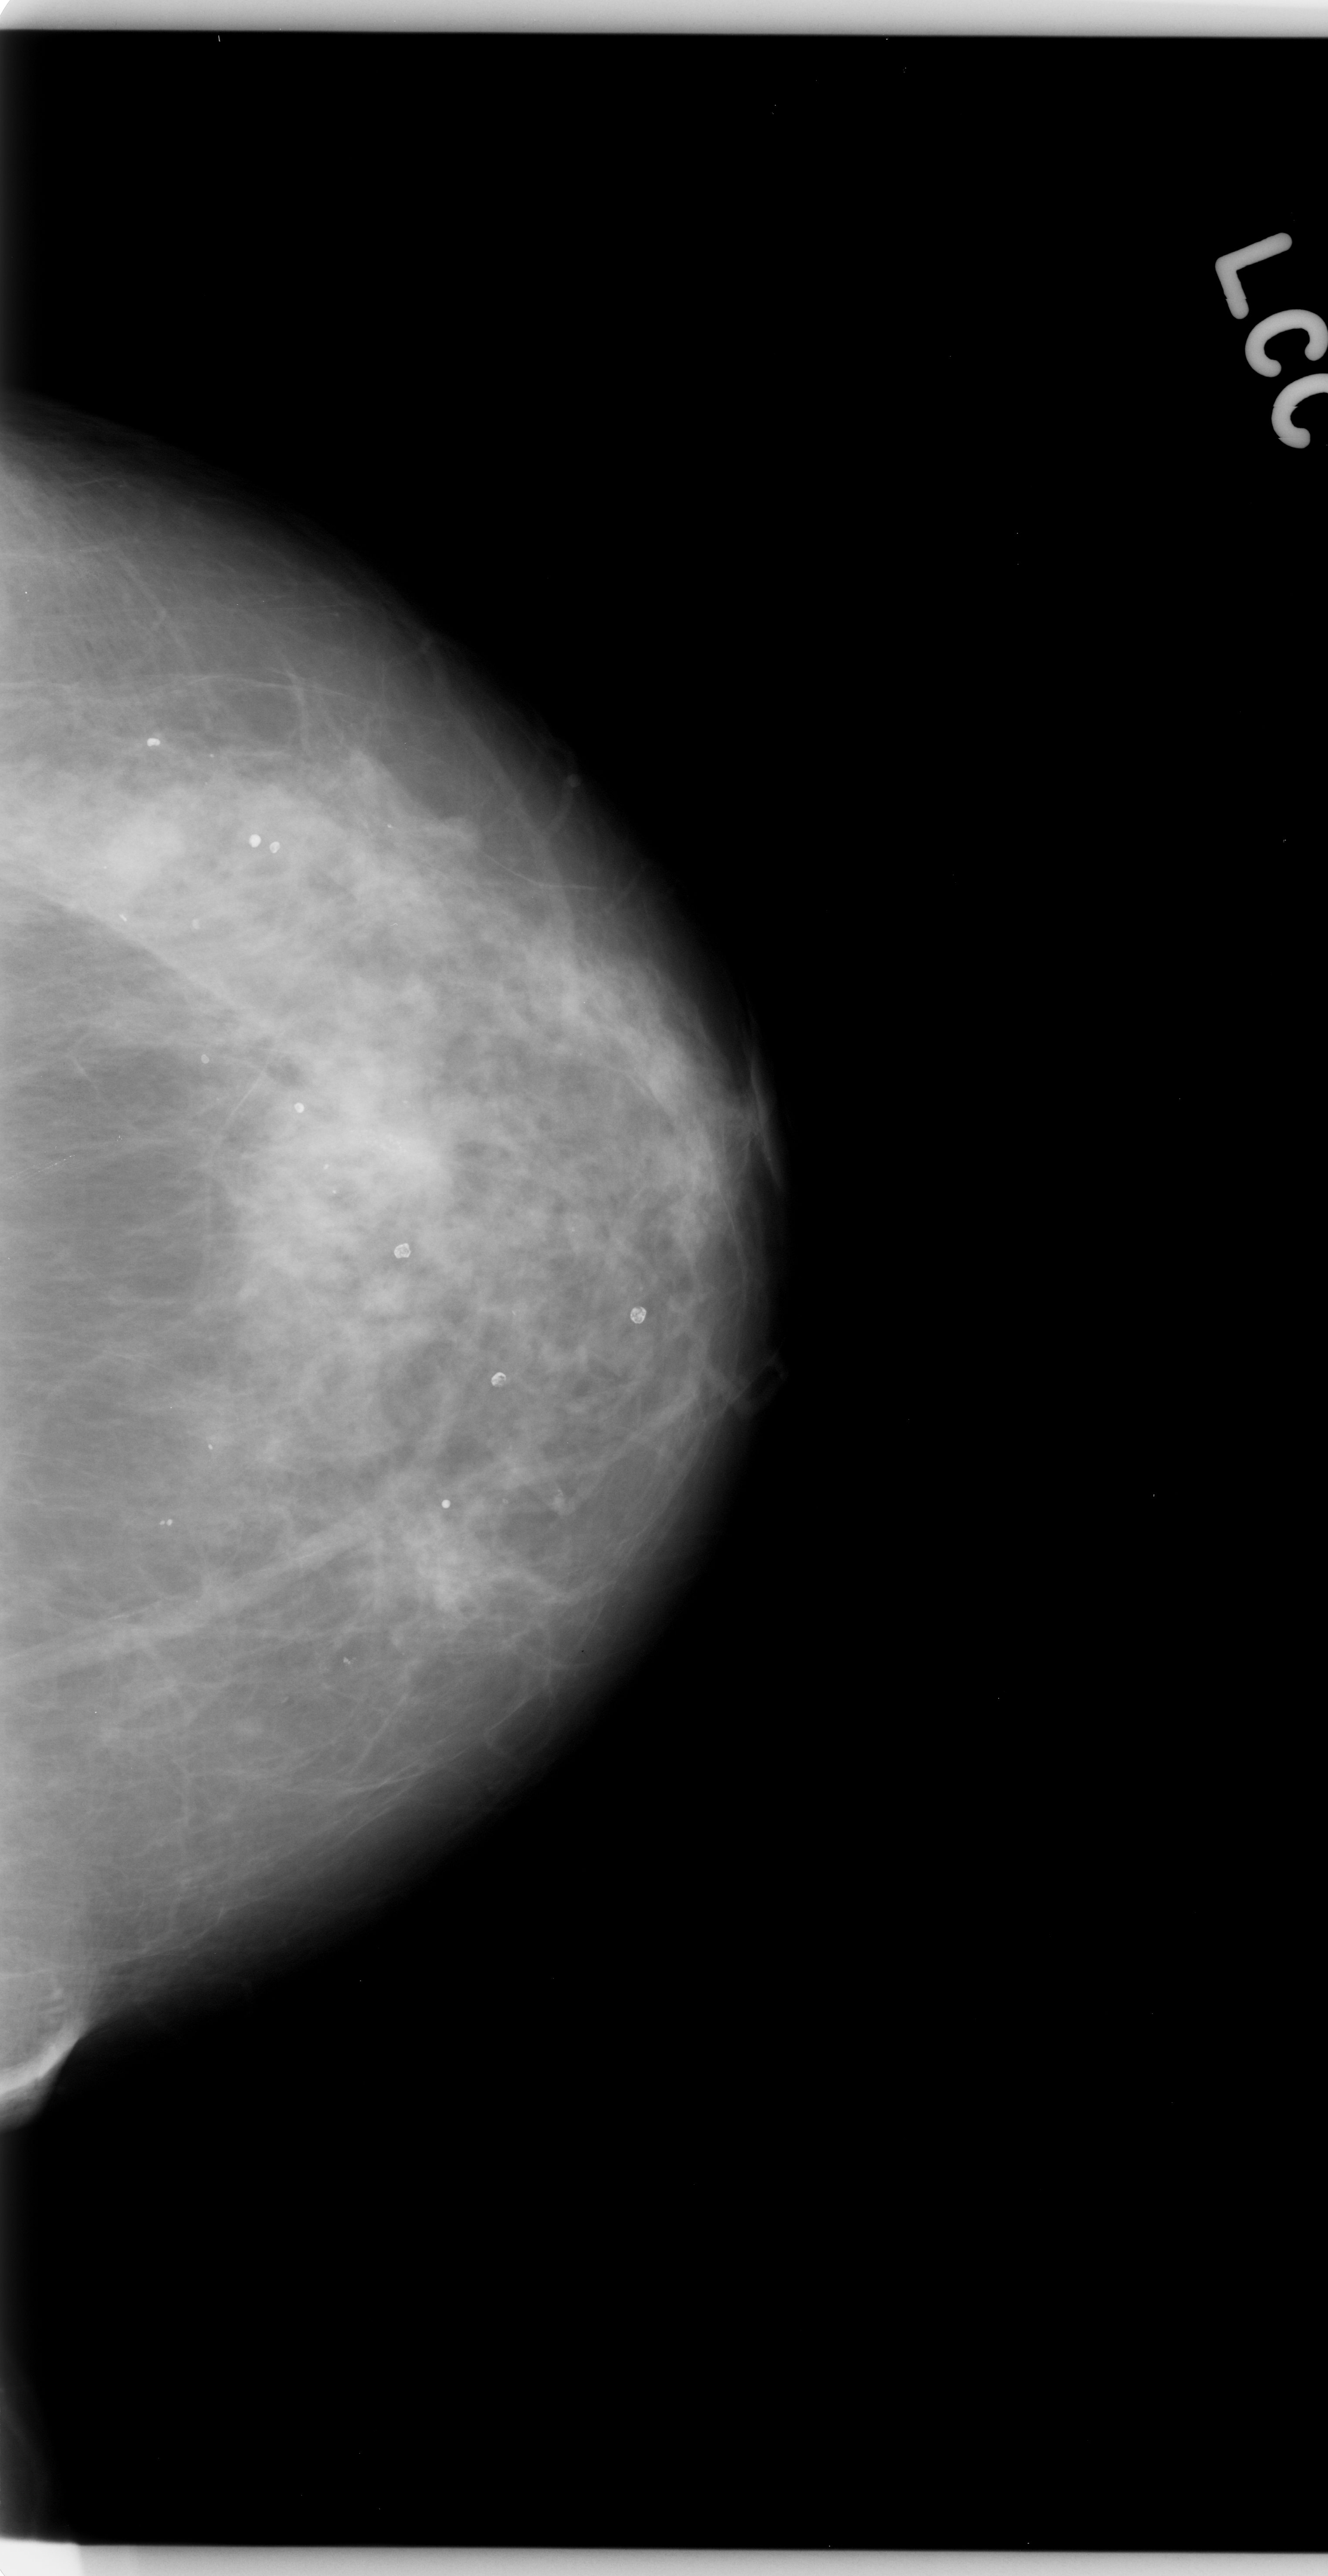
Scanned film-screen mammogram; left breast; CC view; BI-RADS breast density category 2 (scale 1–4).
Abnormality record for this image: calcifications, morphology amorphous, distribution clustered; BI-RADS assessment category 5; subtlety rating 4 on a 1 (subtle) to 5 (obvious) scale; pathology (as recorded): malignant.